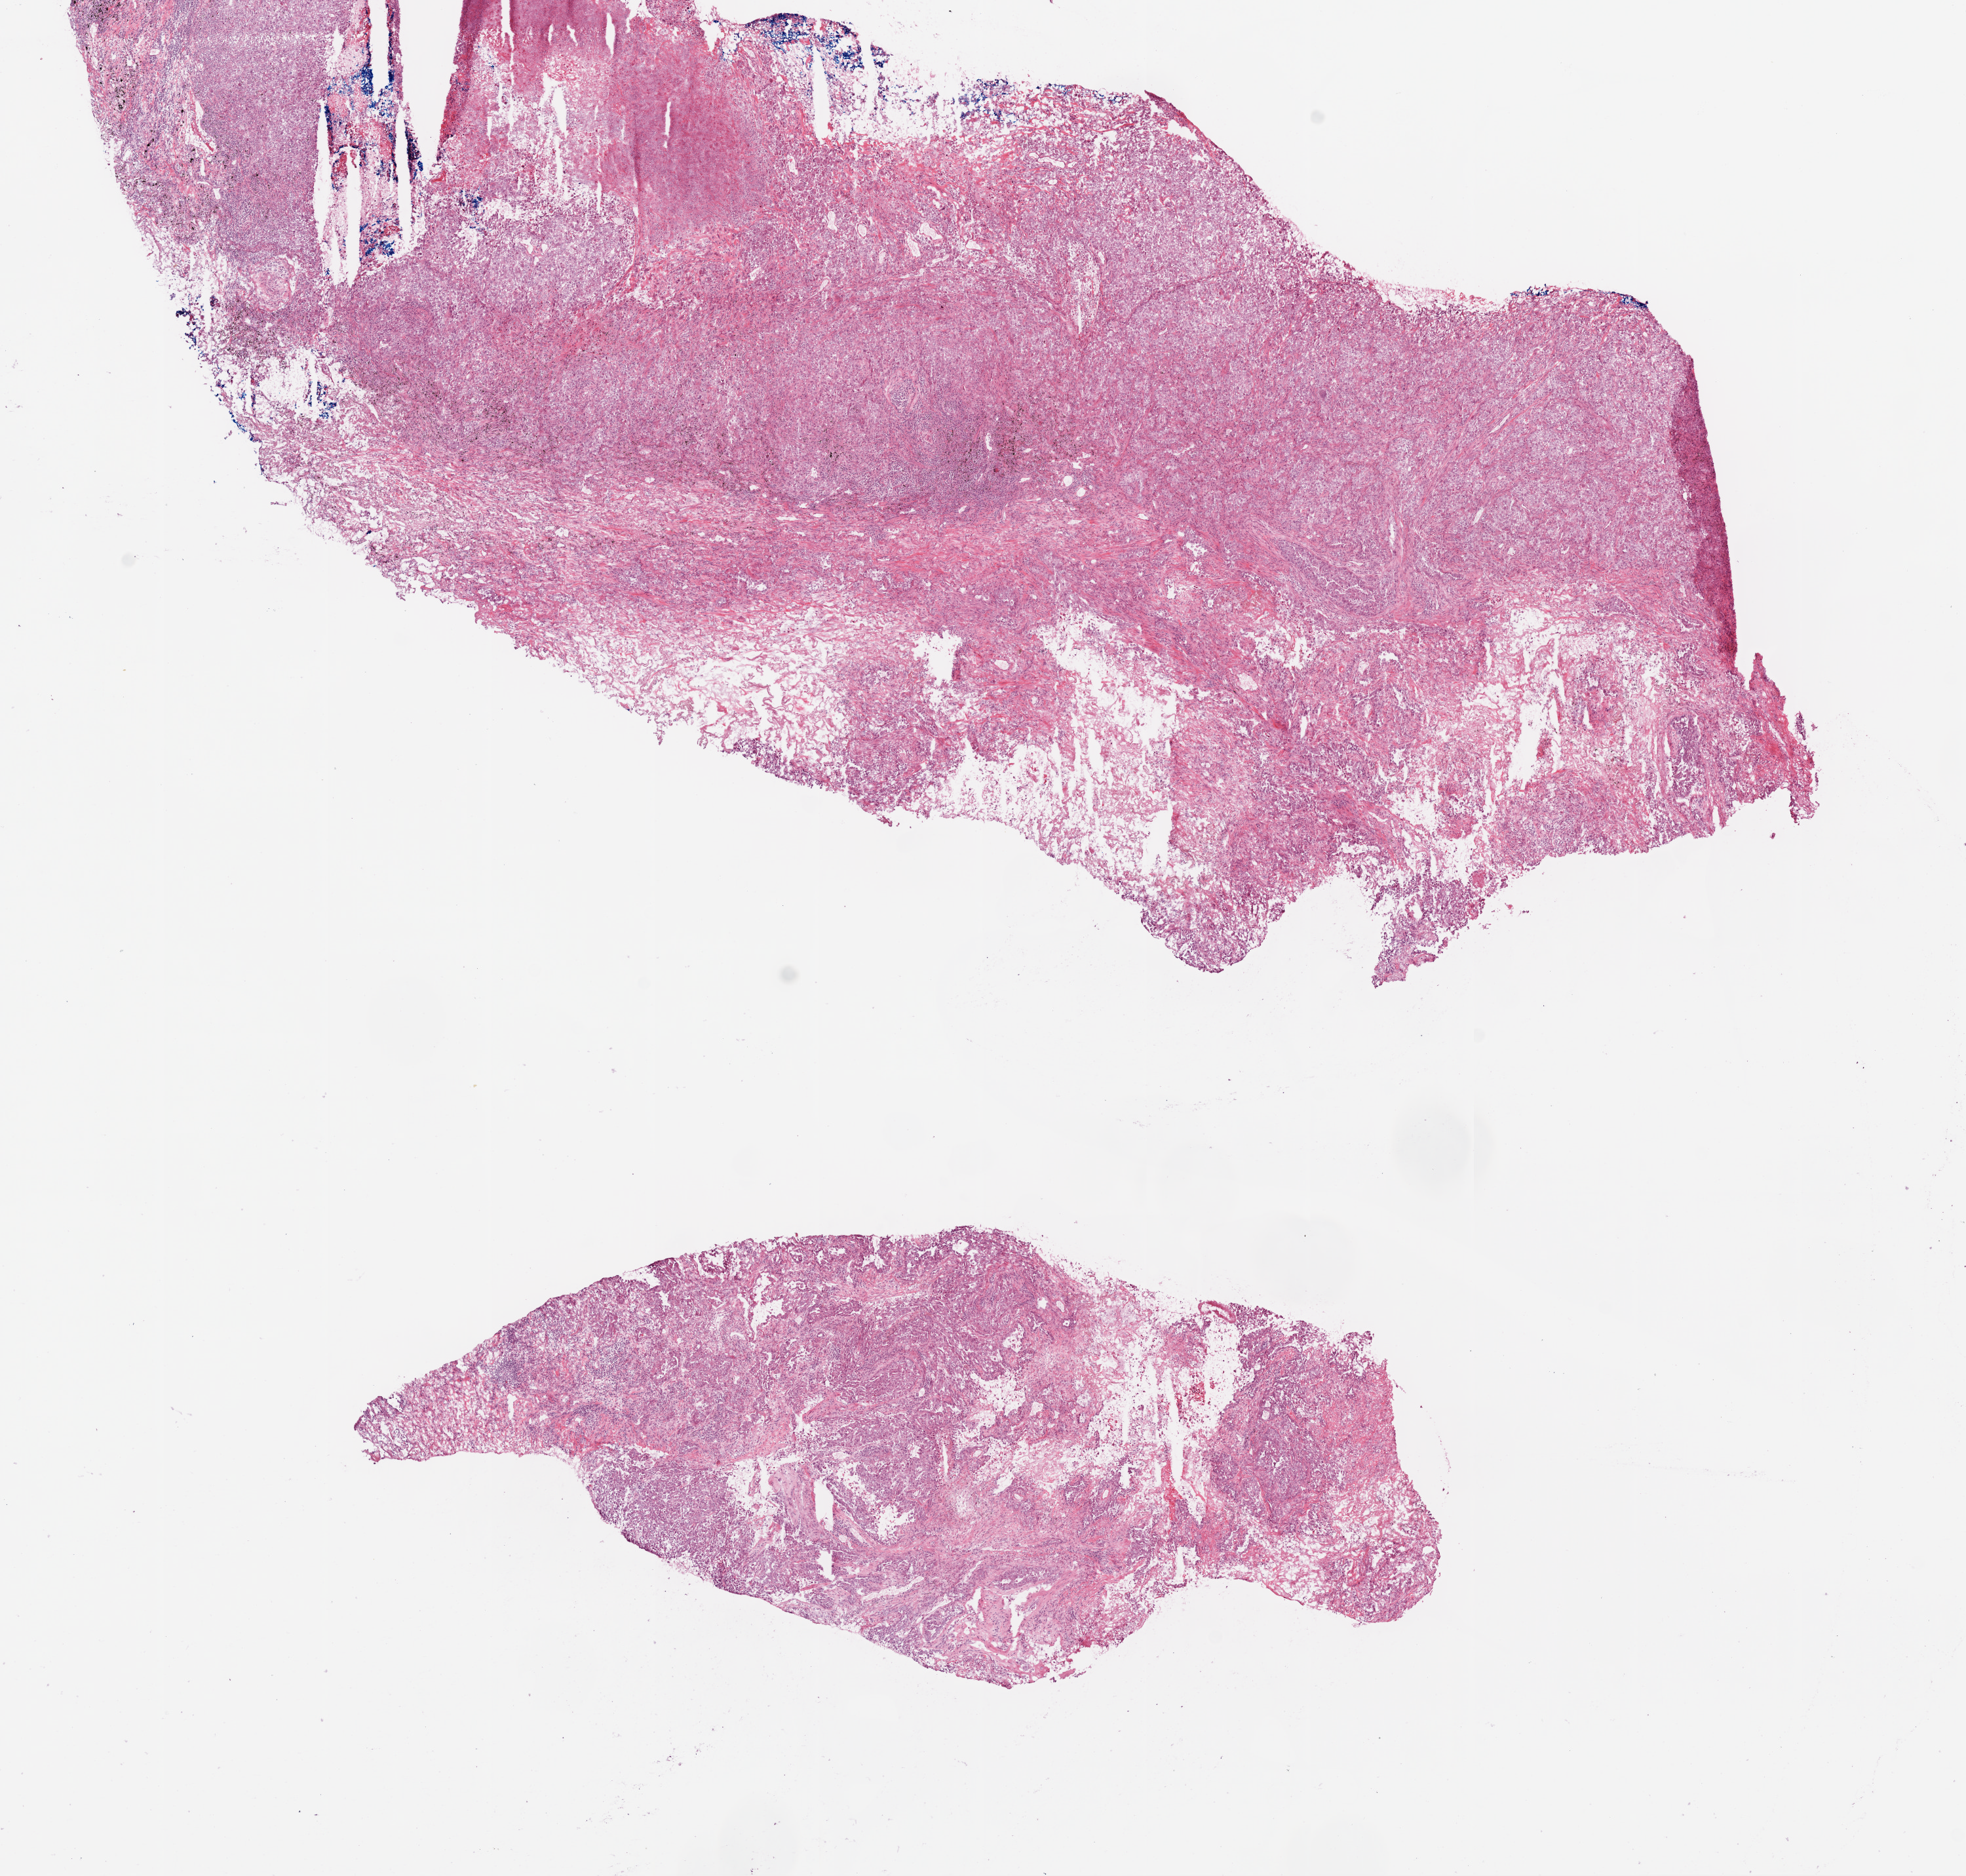
Digitized Hematoxylin and eosin (H&E) stained tissue section (whole slide), whole scanned area (about 12.0 x 11.5 mm, from a 20x scan) shown as a low-resolution overview, frozen section from the bottom of the tissue portion, primary tumour sample from the lung. Male patient; age at initial diagnosis 68 years. Slide review estimates, as recorded: tumour cells 75%, tumour nuclei 70%, normal cells 10%, stromal cells 10%, necrosis 5%.
Pathologic diagnosis: Adenocarcinoma, NOS (upper lobe, lung). AJCC pathologic stage: IIB.